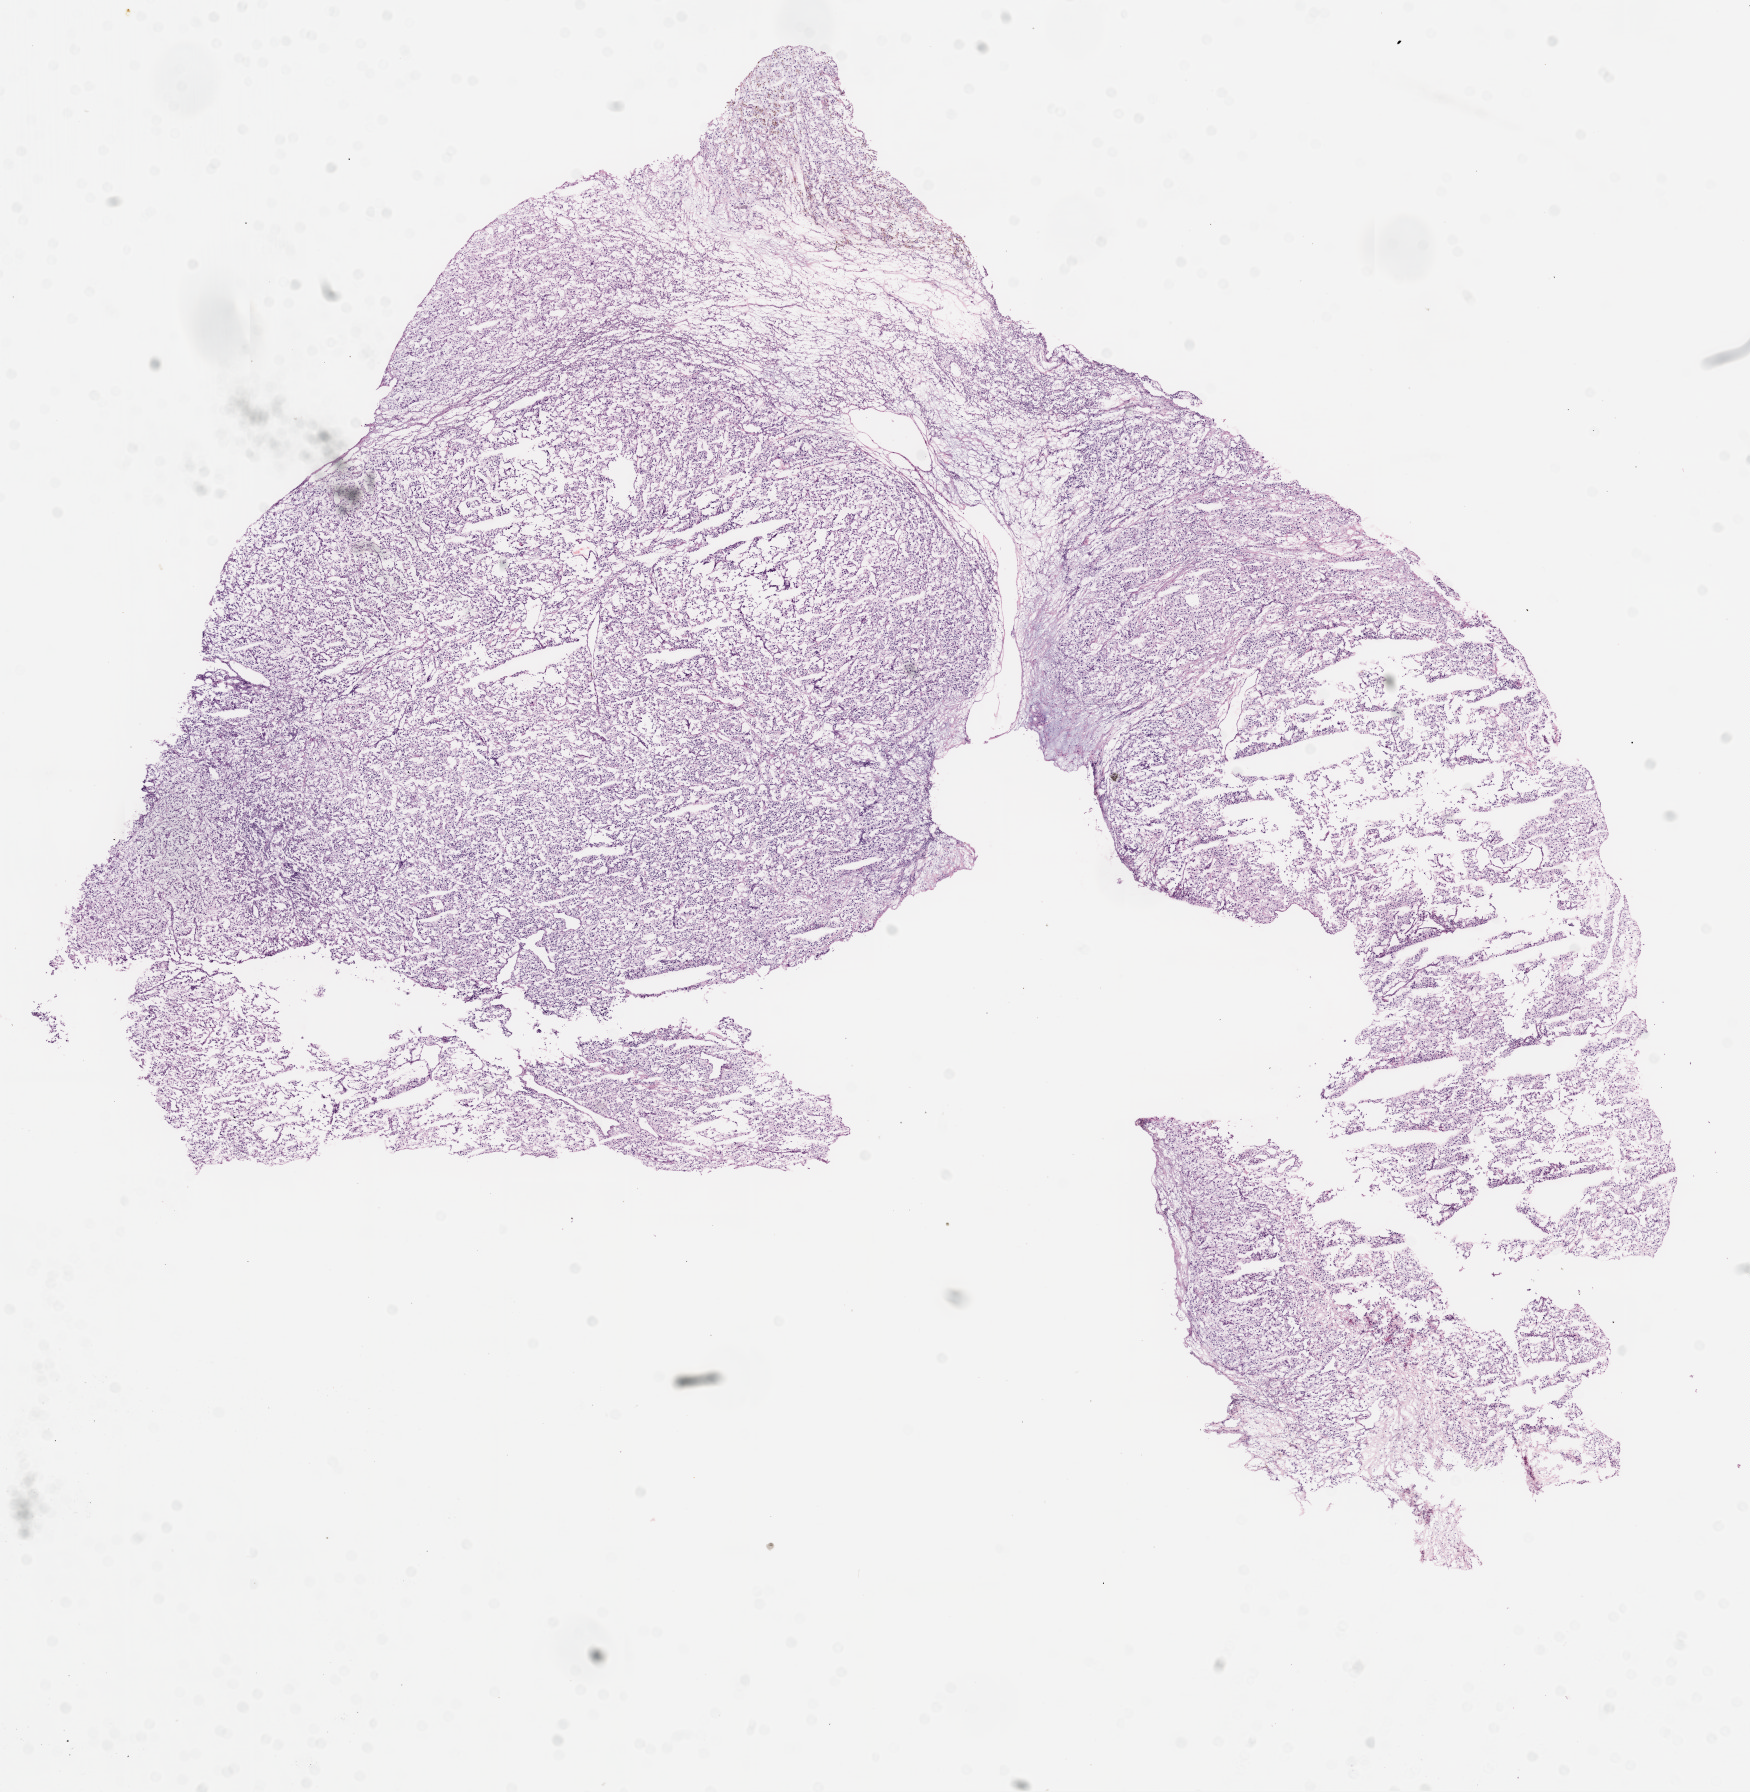
H&E-stained whole-slide image, a low-resolution overview of the entire scanned area, about 14.0 x 14.4 mm (slide scanned at 20x). Frozen section. Kidney, primary tumour sample. Patient: male, age at initial diagnosis 56 years. Histologic grade: G3 (poorly differentiated). Pathologist review of this section (percent, as recorded): tumour cells 90%, tumour nuclei 90%, normal cells 0%, stromal cells 10%, necrosis 0%.
- AJCC pathologic stage: IV
- pathologic diagnosis: Clear cell adenocarcinoma, NOS
- laterality: right
- TNM: T3a N0 M1
- lymph nodes positive (case pathology): 0 of 3 examined